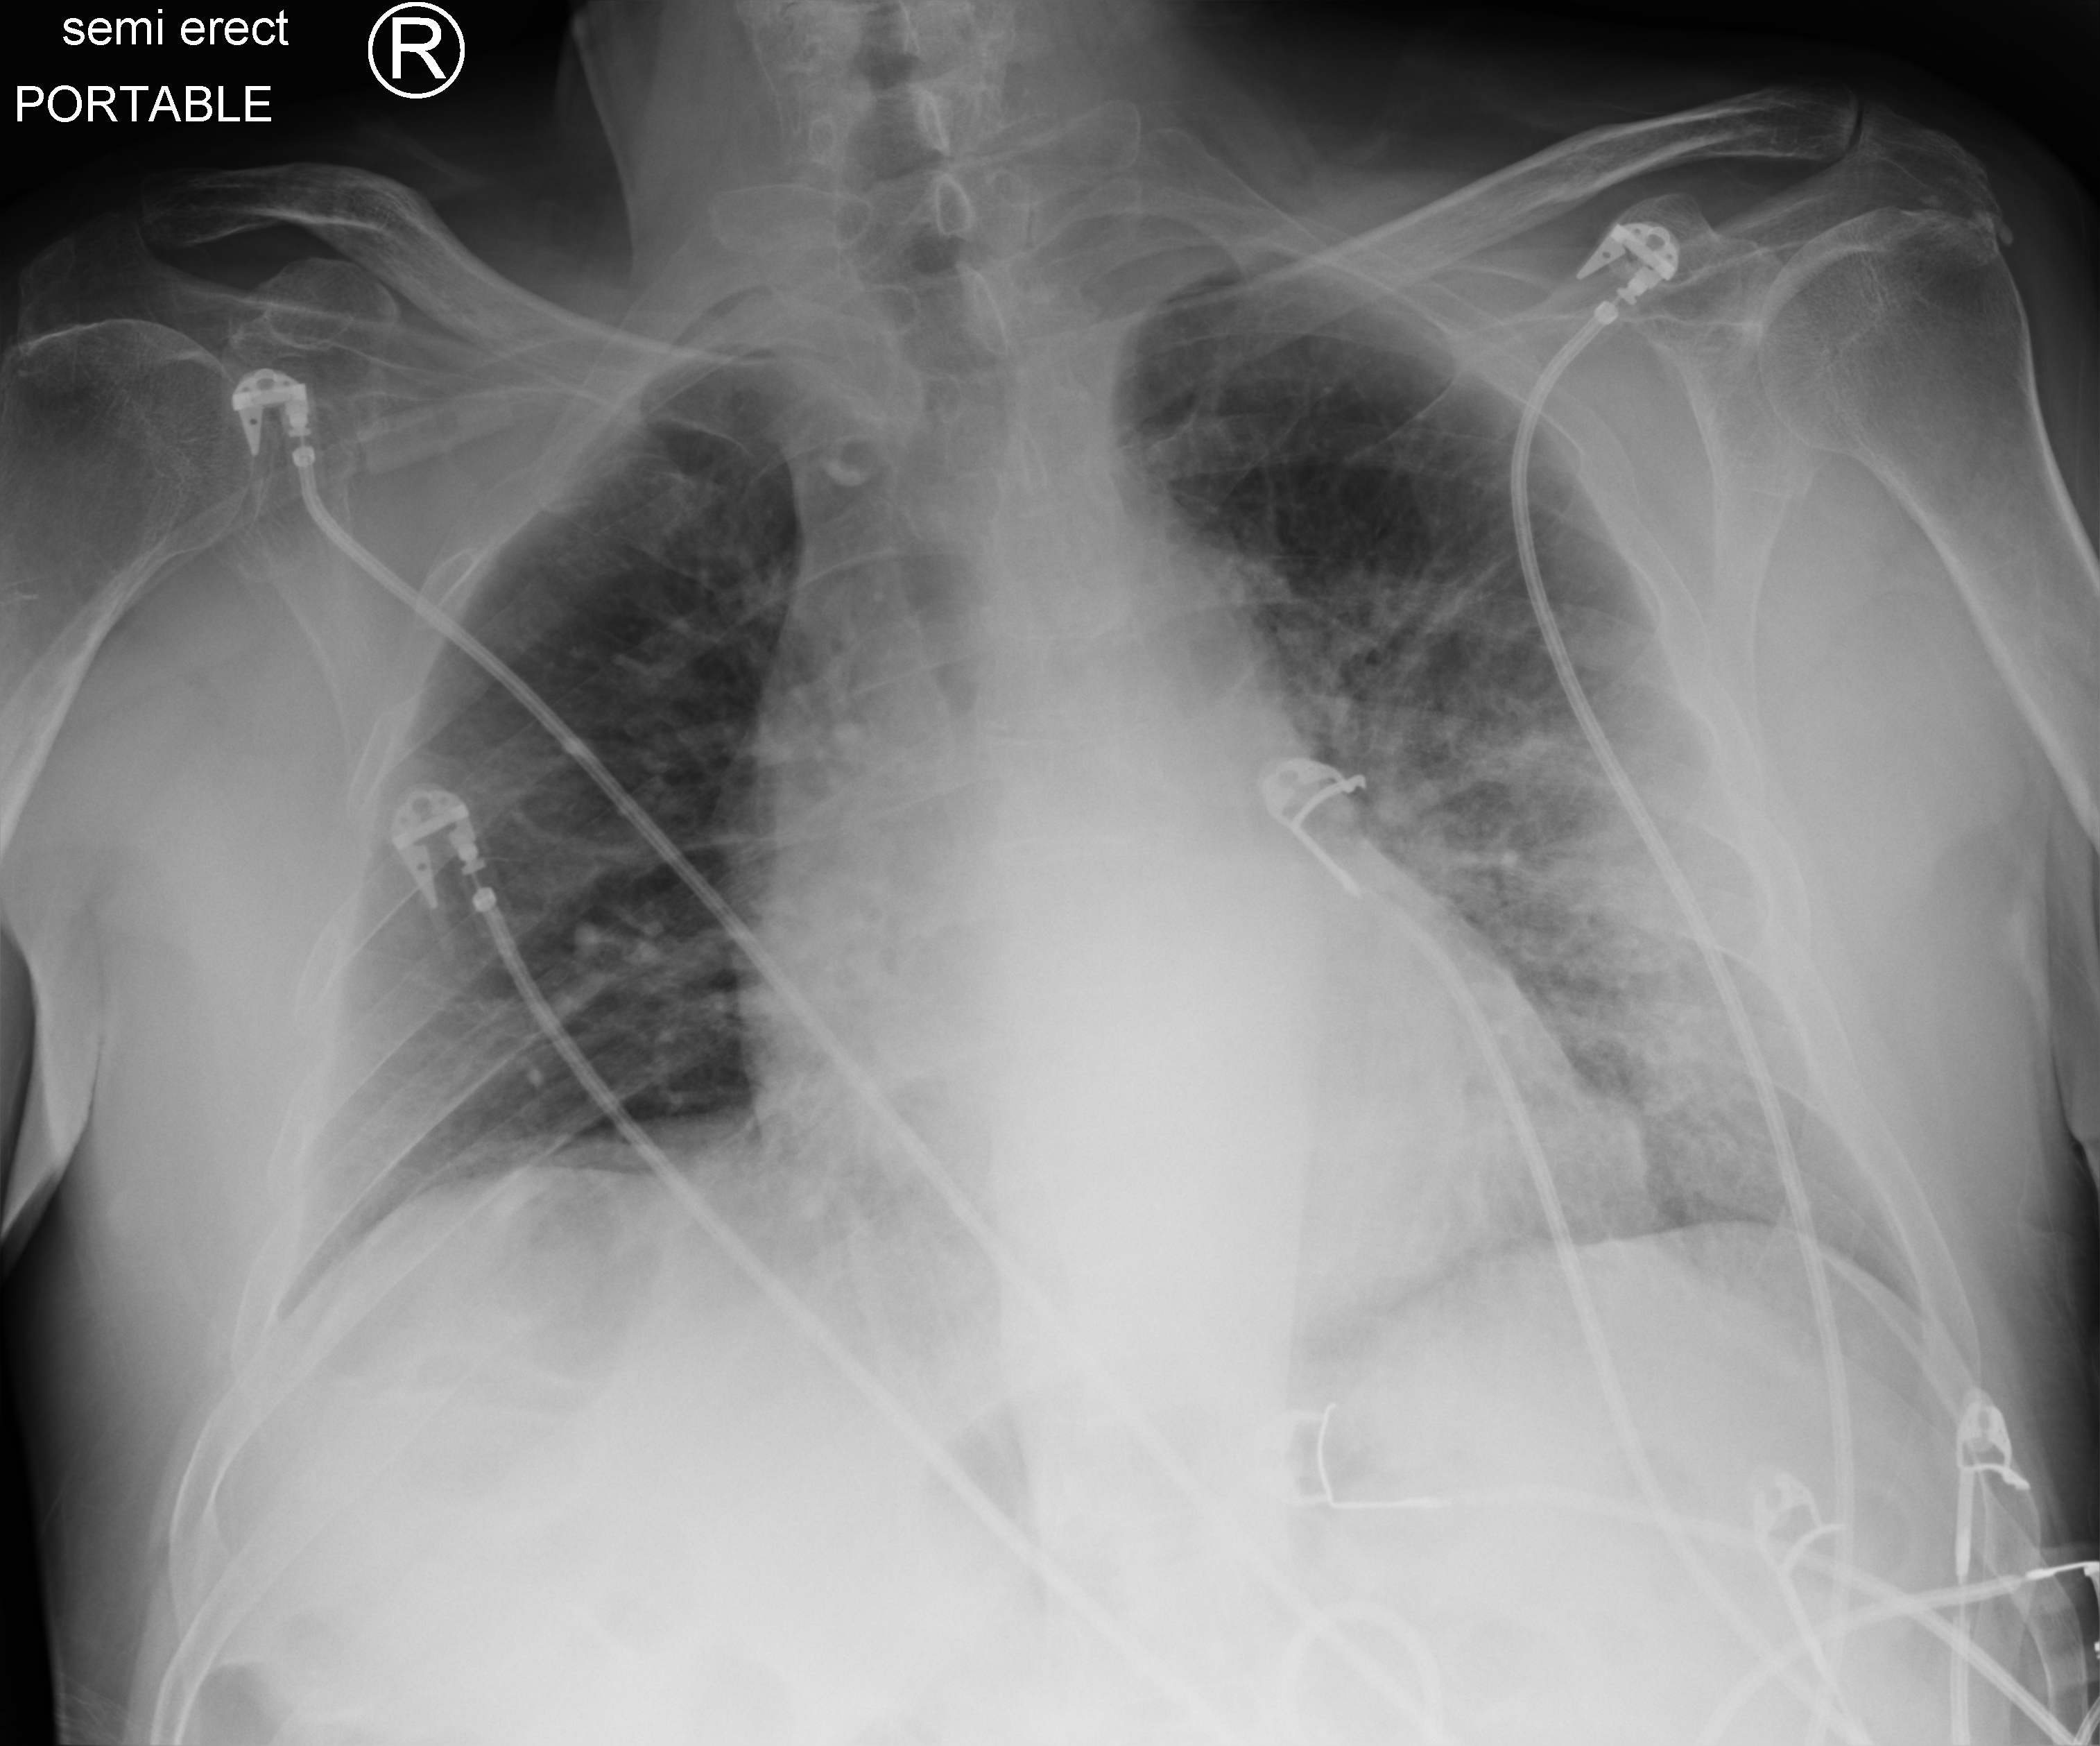
Bedside chest radiograph (computed radiography); anteroposterior (AP) projection. Patient hospitalised with COVID-19; male, aged 60–74 years.
Admission-level facts for this patient (not findings on this image; timing relative to this image not recorded): diabetes (admission record): no; length of hospital stay: 25 days; mechanically ventilated during this hospital stay: yes.